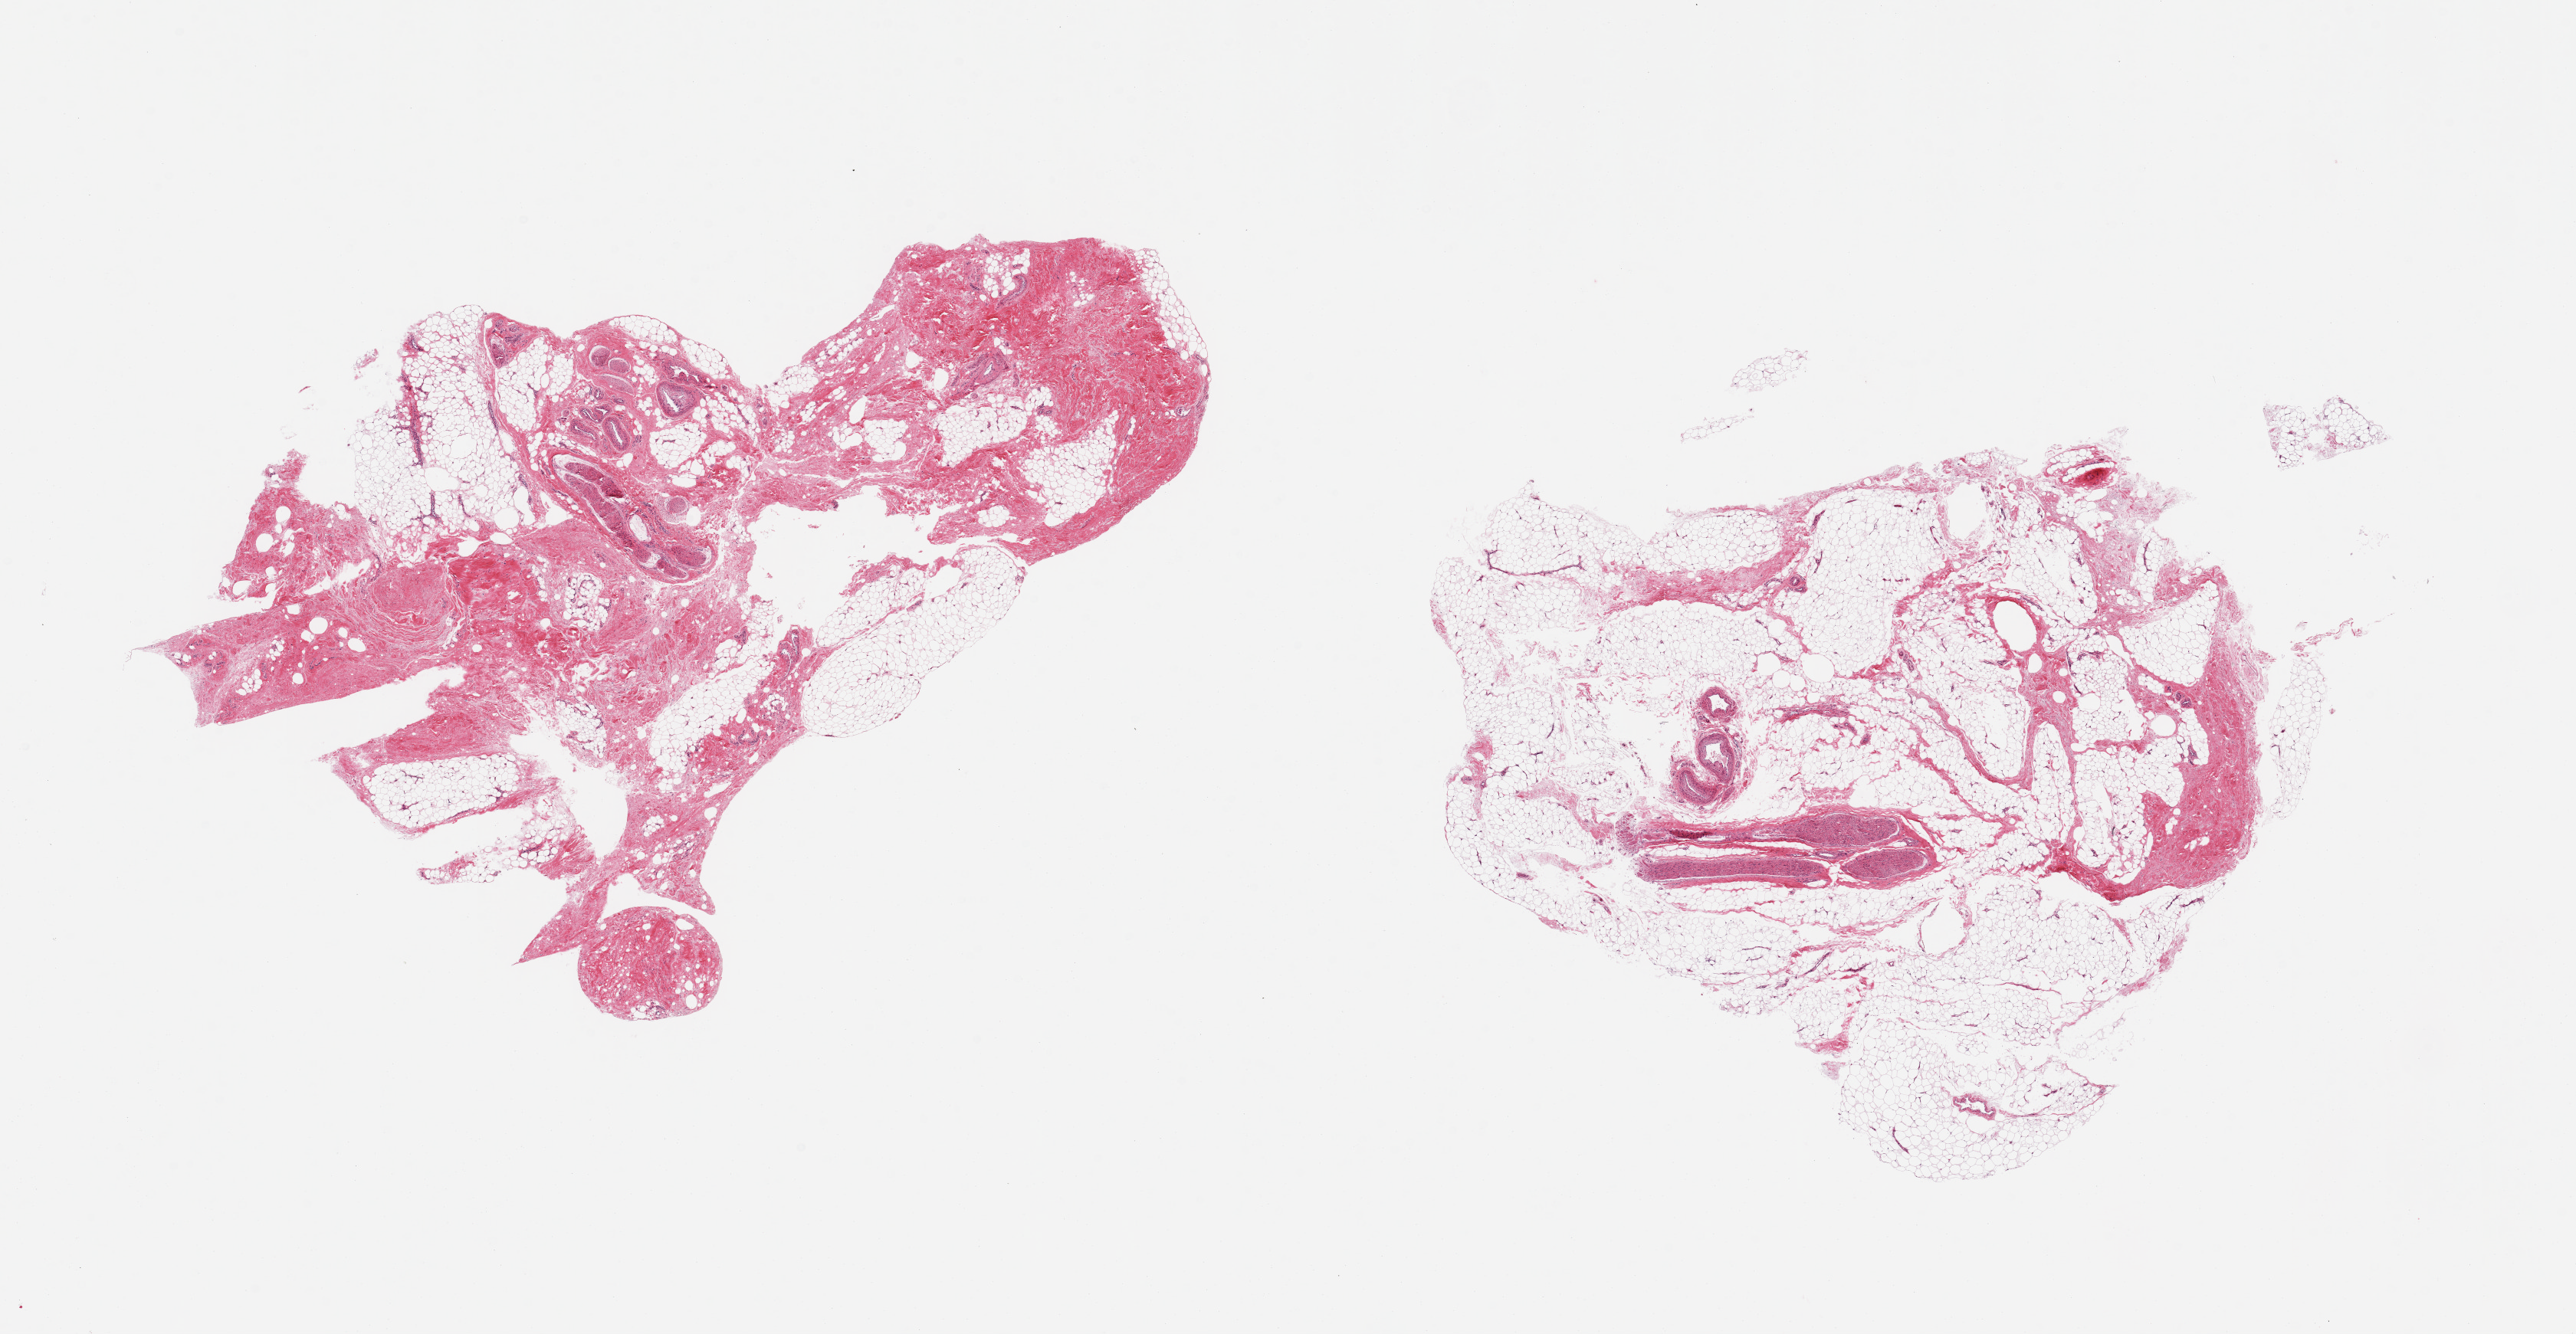
Hematoxylin and eosin (H&E) whole-slide image, brightfield — low-resolution overview of the scanned area, about 26.6 x 13.8 mm (acquisition: 20x scan). PAXgene-fixed paraffin-embedded (PFPE) section. Target tissue: adipose tissue. Tissue donor sample.
Reviewer comment on this tissue sample: 2 pieces; 20% & 60% fibrovascular & neural content.